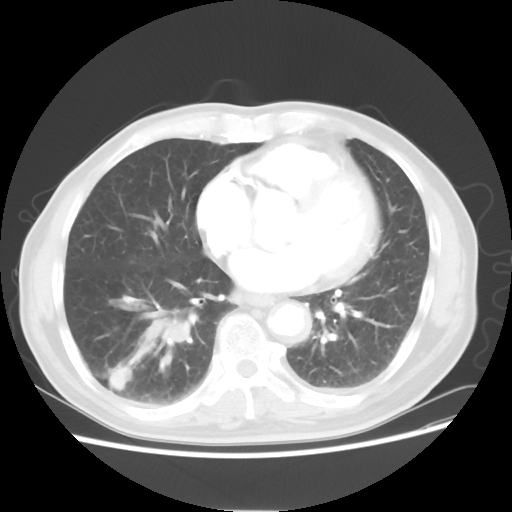
Chest CT, one axial slice. Slice 24 of 58 in the series (ordered by position). Reconstruction kernel STANDARD. 120 kVp. Lung window (W 1500 / L -600 HU). 5 mm slice thickness. 512 × 512 image matrix. Male patient, age 74 years. From the clinical record (not read from this slice): clinical TNM (as recorded): T1c N1 M1.
Outlined on this slice (bounding box drawn by a radiologist):
- lung tumour (recorded histology: adenocarcinoma): bounding box [x1, y1, x2, y2] px = [110, 291, 195, 368]